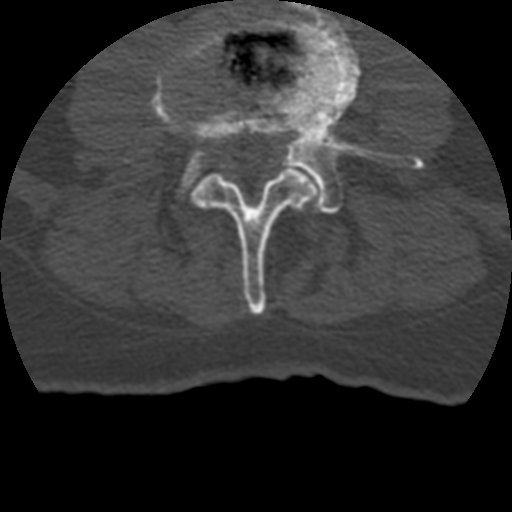
CT including the spine, one axial slice; position 78 of 399 along the scan axis; reconstruction kernel STANDARD; bone window (W 1800 / L 400 HU); 1.25 mm slice thickness; 512 × 512 image matrix, field of view 160 × 160 mm. Patient age 69 years. From the clinical record (not read from this slice): primary cancer: prostate.
Structures marked on this image (semi-automatic segmentation, software-assisted and operator-edited):
- L3 vertebra: box from (x=151, y=28) to (x=317, y=315) px
- L4 vertebra: (x=183, y=4)–(x=425, y=213)